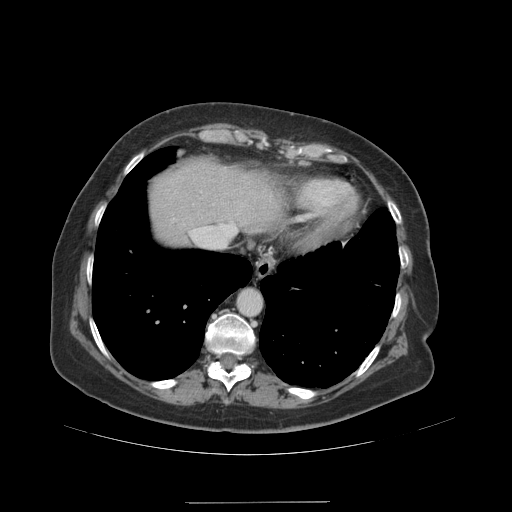
Contrast-enhanced abdominal CT (liver protocol), one axial slice. Slice 85 of 99 in the series (ordered by position). Reconstruction kernel STANDARD. 140 kVp. Soft-tissue window (W 400 / L 40 HU). 2.5 mm slice thickness. 512 × 512 image matrix, field of view 440 × 440 mm. Case-level facts recorded for this patient, not image findings: diagnosis: hepatocellular carcinoma (patient treated with transarterial chemoembolisation; whether this scan precedes or follows treatment is not stated here); TNM stage (as recorded): Stage-IVA; Child-Pugh class: A.
Outlined on this slice (semi-automatically segmented with operator editing):
- abdominal aorta: box from (x=238, y=289) to (x=260, y=315) px
- liver parenchyma outside the tumour (the mass and vessels are separate outlines, so this box may not span the whole liver): (x=150, y=160)–(x=280, y=245)
- liver vessels: (x=189, y=222)–(x=238, y=236)